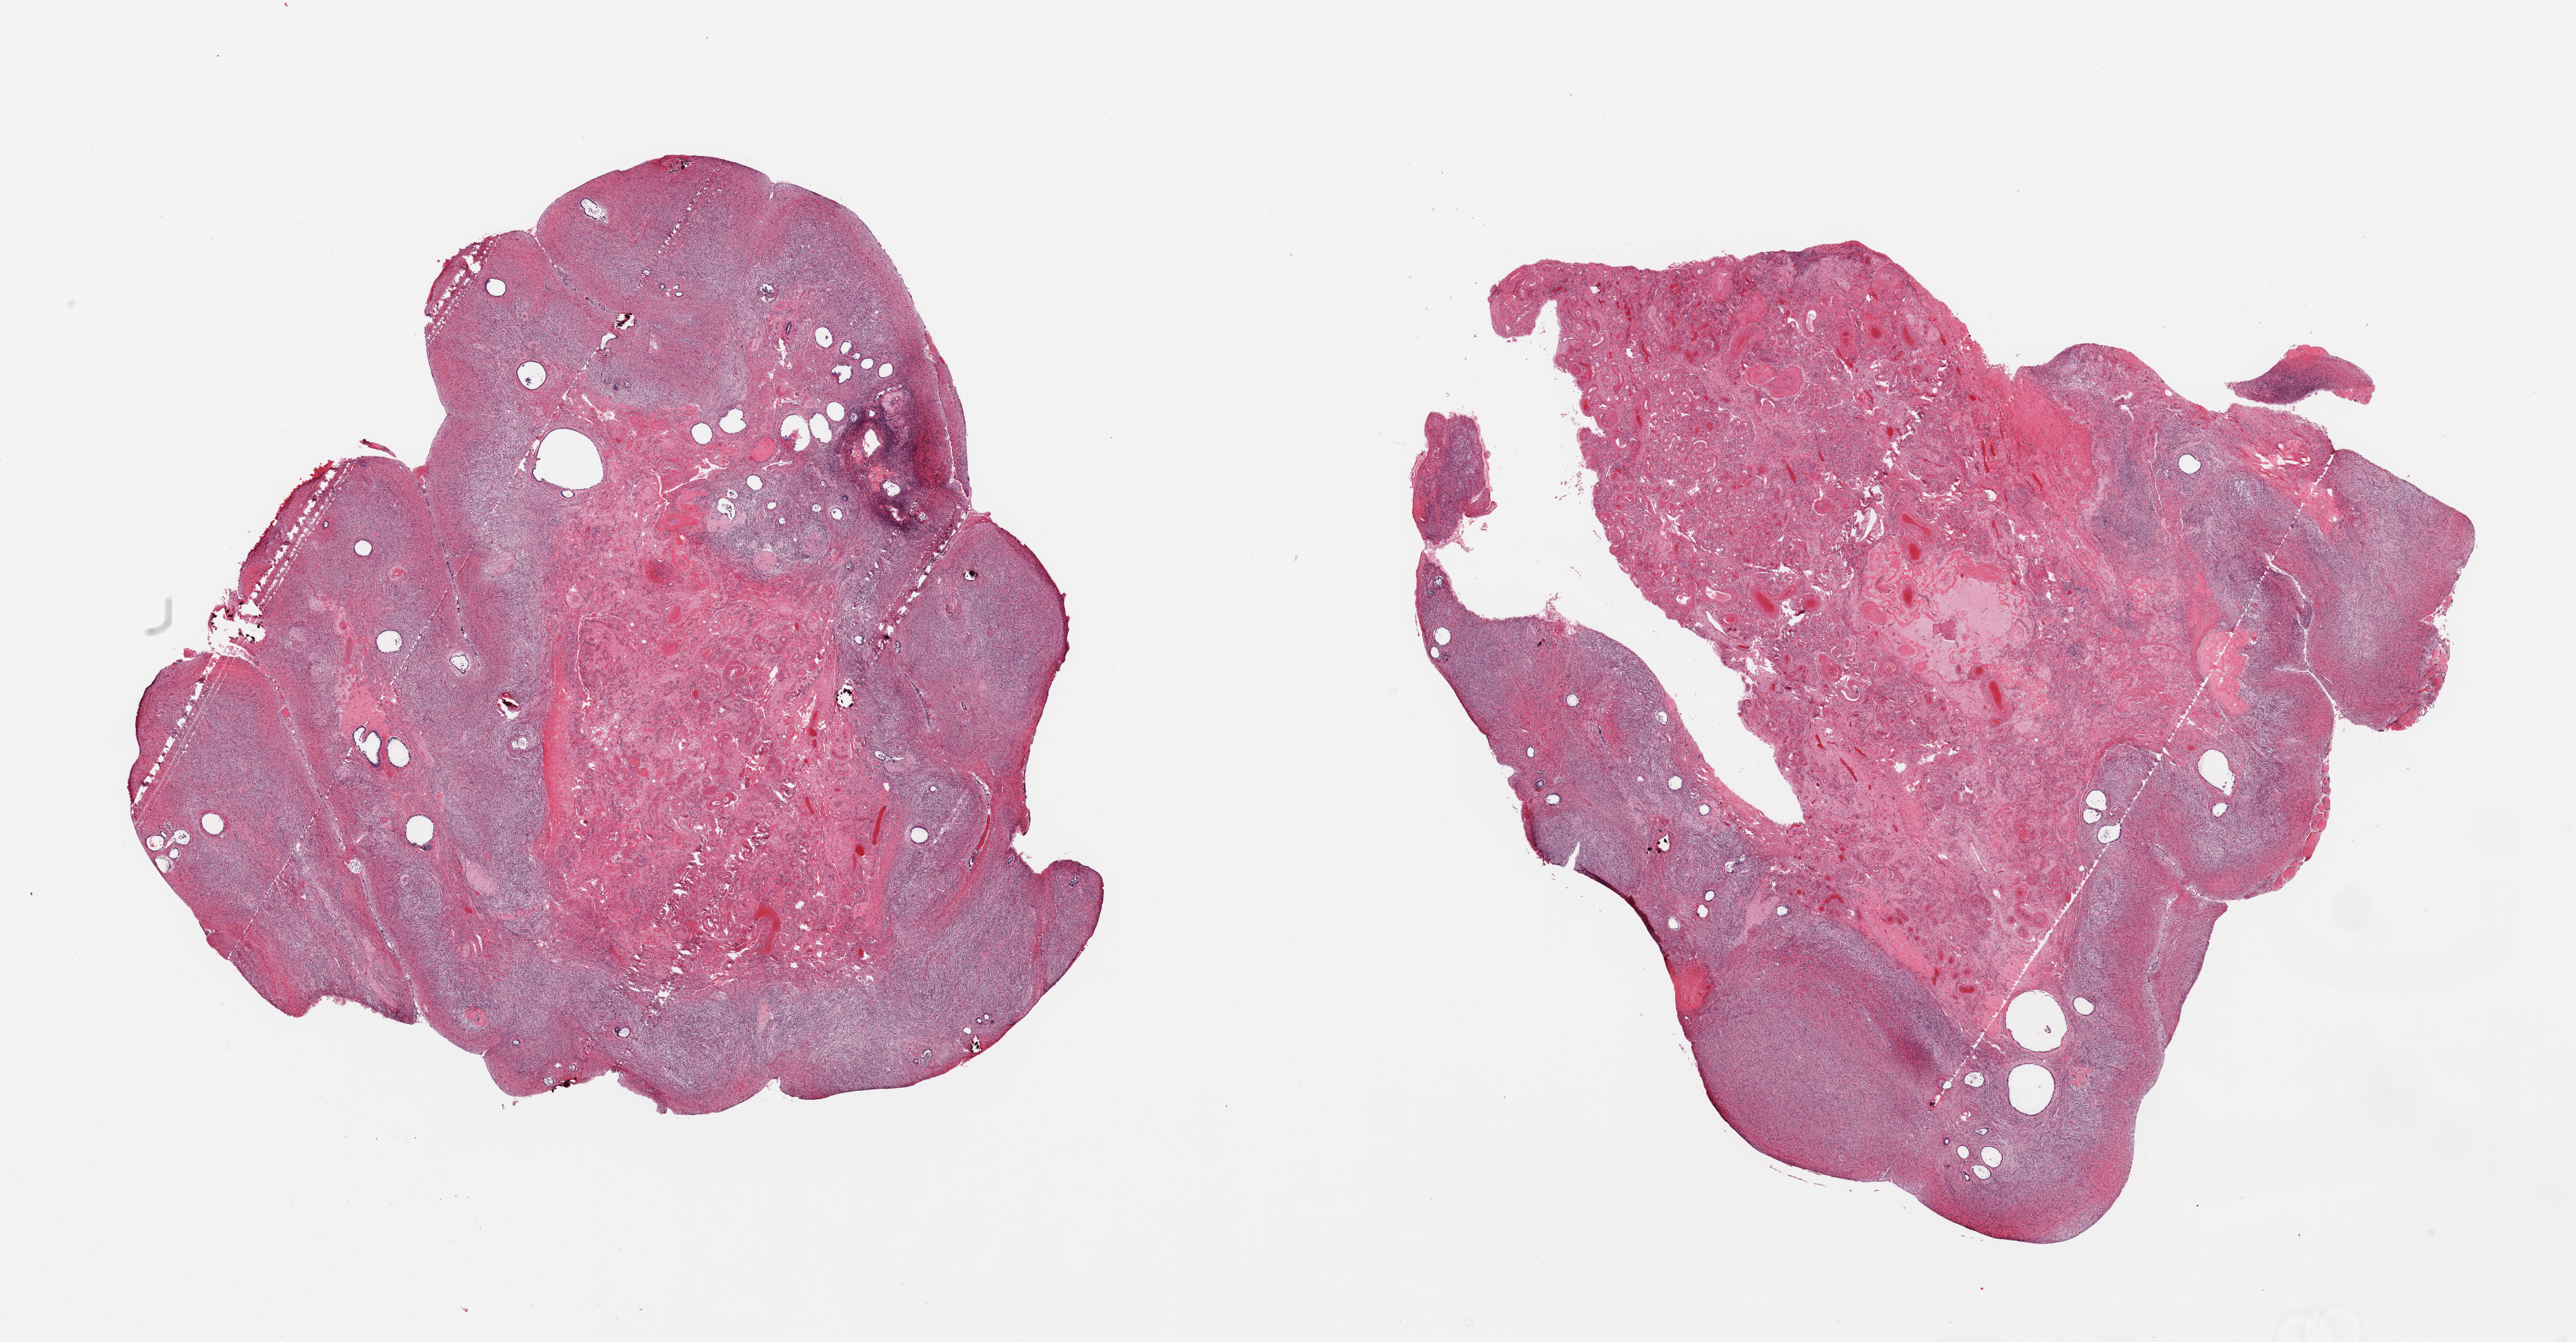
Digitized H&E-stained section — a low-resolution overview of the entire scanned area, about 29.5 x 15.4 mm (from a 20x scan); PAXgene-fixed, paraffin-embedded tissue; section of ovary (target tissue); tissue donor sample.
- pathologist's review note for this sample: 2 pieces, post menopausal atrophy, scattered (sub millimeter) simple cysts